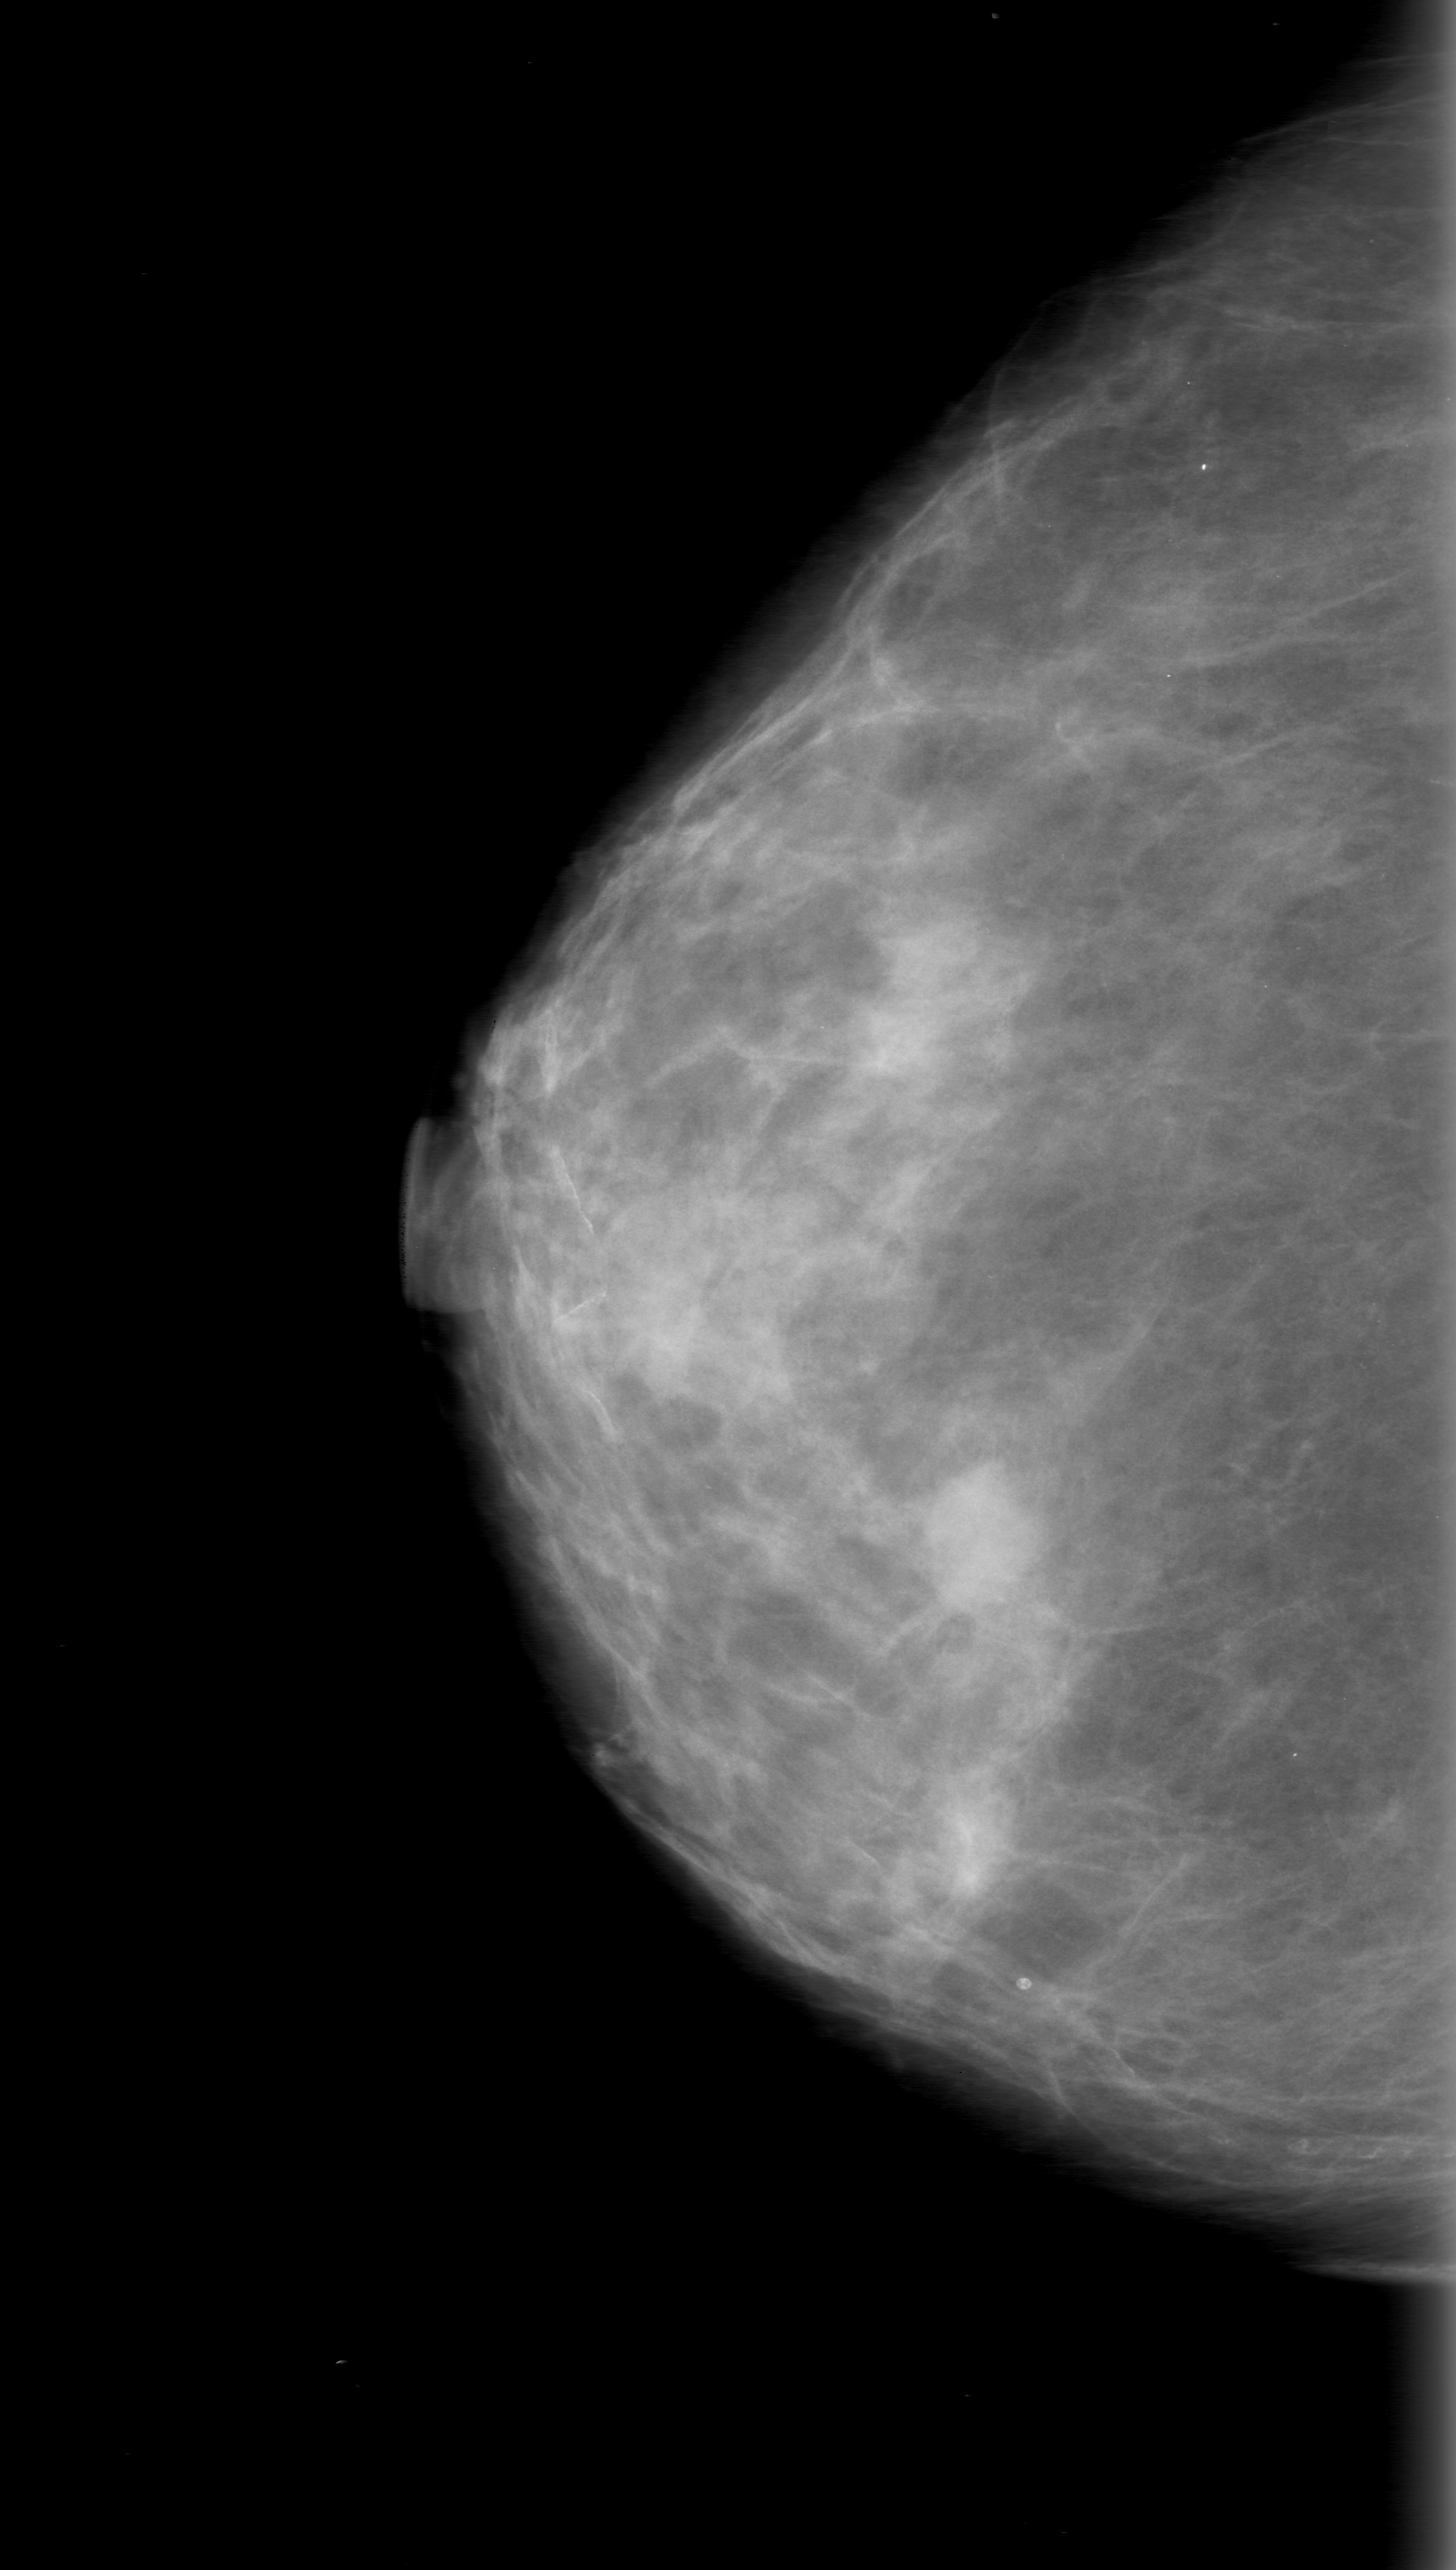
Scanned film-screen mammogram; right breast; CC view; breast composition: scattered fibroglandular densities (BI-RADS density category 2 of 4); 1456 × 2570 image matrix.
Expert-marked regions of interest on this film, with their recorded descriptors:
- mass, shape oval, margins obscured; BI-RADS assessment category 0 (incomplete: needs additional imaging); subtlety rating 5 on a 1 (subtle) to 5 (obvious) scale; pathology (as recorded): benign: bounding box [x1, y1, x2, y2] px = [869, 1452, 1061, 1639]